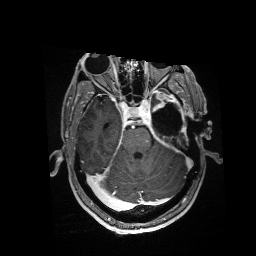
Brain MRI from a brain-tumour surgery series, one axial slice. Slice 110 of 176 in the series (ordered by position). T1-weighted post-contrast. 256 × 256 image matrix. Case-level facts recorded for this patient, not image findings: histopathology: Glioblastoma; WHO grade: 4; IDH mutation: no.
Annotated regions visible in this slice (manually delineated by an expert):
- residual tumour: box from (x=153, y=91) to (x=184, y=118) px